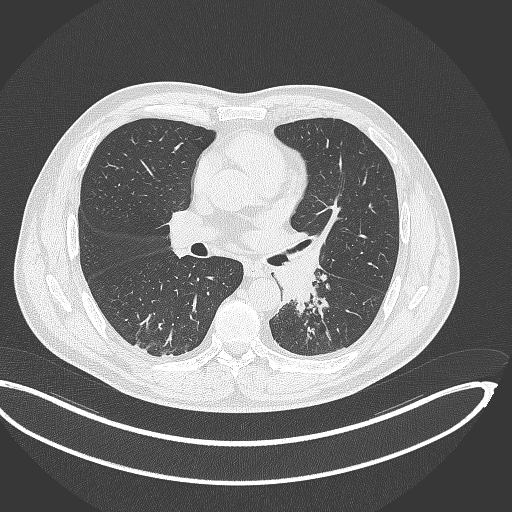
Chest CT, one axial slice; position 193 of 362 along the scan axis; reconstruction kernel B70f; 120 kVp; lung window (W 1500 / L -600 HU); 512 × 512 image matrix. Patient: male, 50 years. Case-level facts recorded for this patient, not image findings: clinical TNM (as recorded): T2a N3 M0.
Structures marked on this image (rectangle marked by the reading radiologist):
- lung tumour (recorded histology: squamous cell carcinoma): bounding box <270,245,324,316> (left, top, right, bottom; pixels)